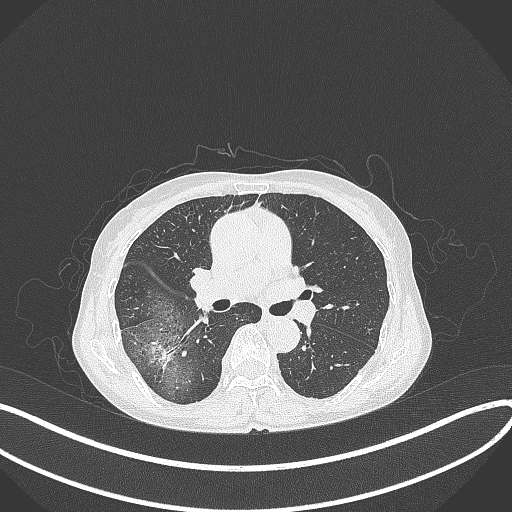
Chest CT, one axial slice; slice 229 of 371 in the series (ordered by position); reconstruction kernel B70f; 120 kVp; lung window (W 1500 / L -600 HU); 1 mm slice thickness; 512 × 512 image matrix. Female patient, age 69 years. From the clinical record (not read from this slice): clinical TNM (as recorded): T1b N0 M0; histopathological grade: G2-3.
Annotated regions visible in this slice (bounding box drawn by a radiologist):
- lung tumour (recorded histology: adenocarcinoma): bounding box (x1, y1, x2, y2) in pixels: (138, 331, 178, 373)